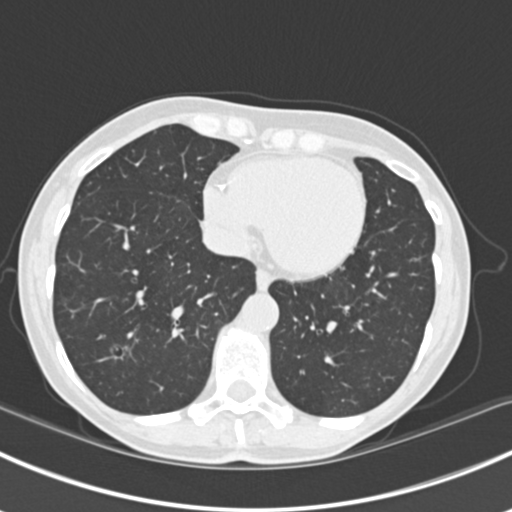
Low-dose screening chest CT, axial slice. Baseline annual screen. Lung window (W 1500 / L -600 HU). Slice 134 of 224 in the series. 512 × 512 image matrix, field of view 310 × 310 mm. Female participant, aged 63 years at enrolment.
Lesion marked by an expert reader, box from (x=96, y=326) to (x=146, y=371) px. The screening reader recorded 10 non-calcified nodules or masses ≥4 mm on this exam; which of them this box marks is not recorded. Official screen result: positive, change unspecified: nodule(s) >= 4 mm or enlarging nodule(s), mass(es), or other non-specific abnormalities suspicious for lung cancer. Later outcome: lung cancer diagnosed 751 days after this screen (after the third annual screen) — bronchiolo-alveolar adenocarcinoma, NOS, right upper lobe, right middle lobe, right lower lobe, left upper lobe, left lower lobe, moderately differentiated (G2), stage IV (AJCC 6th edition).